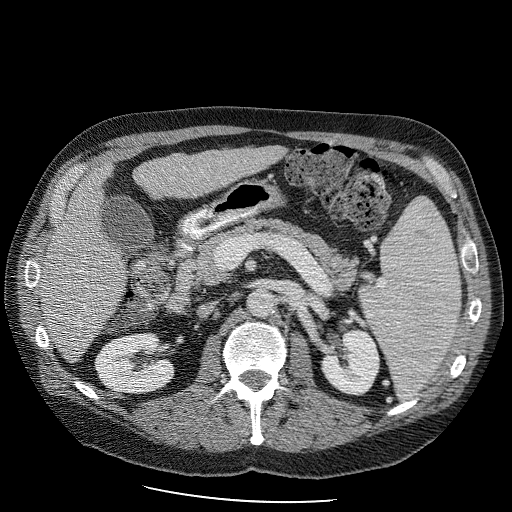
Contrast-enhanced abdominal CT (liver protocol), one axial slice. Slice 39 of 98 in the series (ordered by position). Reconstruction kernel STANDARD. Soft-tissue window (W 400 / L 40 HU). 2.5 mm slice thickness. 512 × 512 image matrix, field of view 400 × 400 mm. From the clinical record (not read from this slice): diagnosis: hepatocellular carcinoma (patient treated with transarterial chemoembolisation; whether this scan precedes or follows treatment is not stated here); TNM stage (as recorded): Stage-II; Child-Pugh class: B; tumour differentiation: moderately differentiated.
Annotated regions visible in this slice (semi-automatic segmentation, software-assisted and operator-edited):
- liver parenchyma outside the tumour (the mass and vessels are separate outlines, so this box may not span the whole liver): bounding box <36,142,291,360> (left, top, right, bottom; pixels)